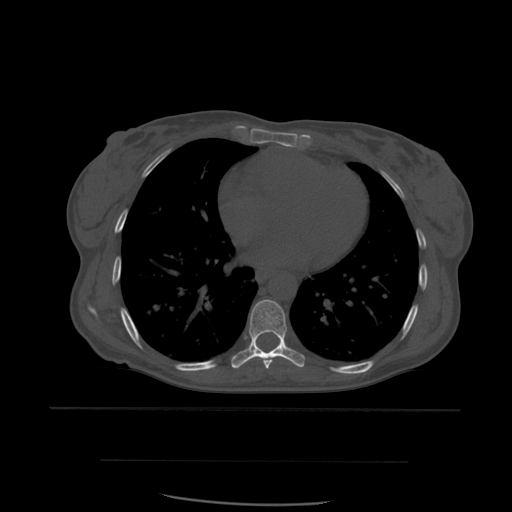
CT including the spine, one axial slice. Position 359 of 574 along the scan axis. Bone window (W 1800 / L 400 HU). 1.25 mm slice thickness. 512 × 512 image matrix. Patient age 48 years. Case-level facts recorded for this patient, not image findings: primary cancer: lung; vertebrae with lytic lesions (as recorded): T11.
Annotated regions visible in this slice (semi-automatically segmented with operator editing):
- T6 vertebra: box from (x=251, y=335) to (x=254, y=339) px
- T7 vertebra: (x=264, y=360)–(x=273, y=369)
- T8 vertebra: (x=231, y=300)–(x=305, y=369)